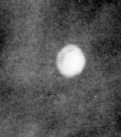
Region of interest cut from a scanned film mammogram (one marked finding); right breast; MLO view.
Calcifications, morphology round and regular / lucent center; BI-RADS assessment category 2; benign; no additional work-up was recommended (benign without callback).